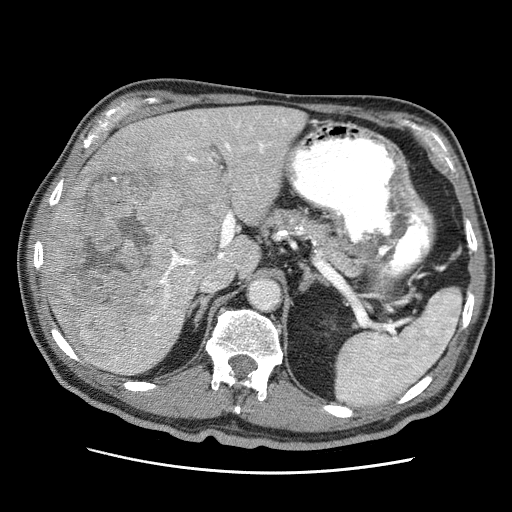
Contrast-enhanced abdominal CT (liver protocol), one axial slice. Position 31 of 75 along the scan axis. Reconstruction kernel STANDARD. 120 kVp. Soft-tissue window (W 400 / L 40 HU). 2.5 mm slice thickness. 512 × 512 image matrix. Case-level facts recorded for this patient, not image findings: diagnosis: hepatocellular carcinoma (patient treated with transarterial chemoembolisation; whether this scan precedes or follows treatment is not stated here); TNM stage (as recorded): Stage-IIIA; Child-Pugh class: A.
Annotated regions visible in this slice (semi-automatic segmentation, software-assisted and operator-edited):
- liver parenchyma outside the tumour (the mass and vessels are separate outlines, so this box may not span the whole liver): box from (x=42, y=106) to (x=306, y=374) px
- mass: (x=48, y=136)–(x=233, y=363)
- liver vessels: (x=133, y=118)–(x=287, y=361)